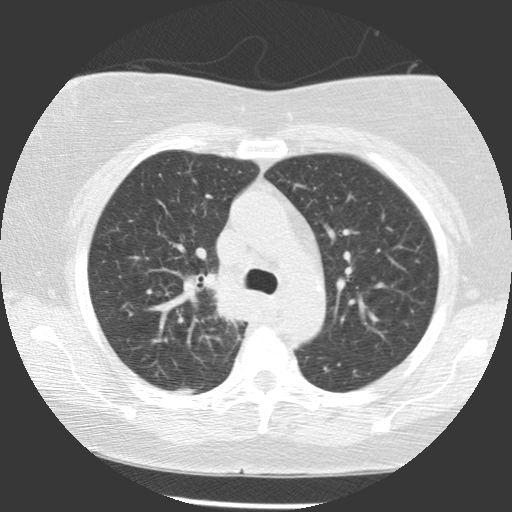
Low-dose screening chest CT, axial slice. First (baseline) screen. Lung window (W 1500 / L -600 HU). 2.5 mm slice thickness. Standard (soft-tissue) reconstruction kernel (STANDARD). Slice 81 of 116 in the series. Female participant, aged 63 years at enrolment.
Expert reader's lesion annotation, bounding box [x1, y1, x2, y2] px = [188, 262, 250, 323]. Reader record for this screening exam (exam-level; its link to the box is not recorded): non-calcified nodule or mass ≥4 mm, right upper lobe, 39 × 36 mm, spiculated (stellate) margins, soft tissue attenuation.